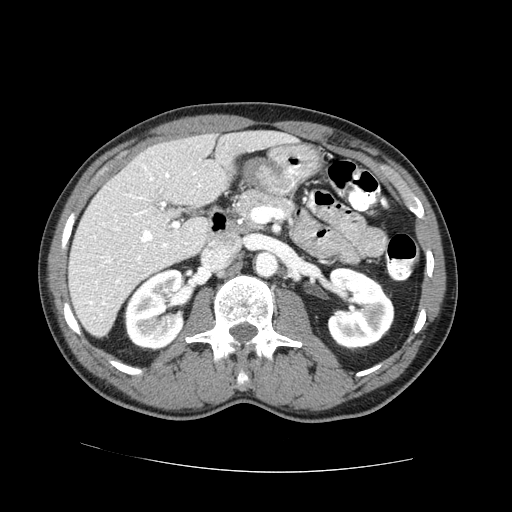
Contrast-enhanced abdominal CT (liver protocol), one axial slice; position 33 of 73 along the scan axis; reconstruction kernel STANDARD; 100 kVp; one of 2 acquisitions stored at this slice position; soft-tissue window (W 400 / L 40 HU); 512 × 512 image matrix, field of view 380 × 380 mm. From the clinical record (not read from this slice): diagnosis: hepatocellular carcinoma (patient treated with transarterial chemoembolisation; whether this scan precedes or follows treatment is not stated here); TNM stage (as recorded): Stage-IVA; Child-Pugh class: A; tumour differentiation: no biopsy; tumour nodularity: uninodular.
Annotated regions visible in this slice (semi-automatic segmentation, software-assisted and operator-edited):
- liver parenchyma outside the tumour (the mass and vessels are separate outlines, so this box may not span the whole liver): bounding box (x1, y1, x2, y2) in pixels: (68, 130, 296, 336)
- liver vessels: (89, 165, 201, 305)